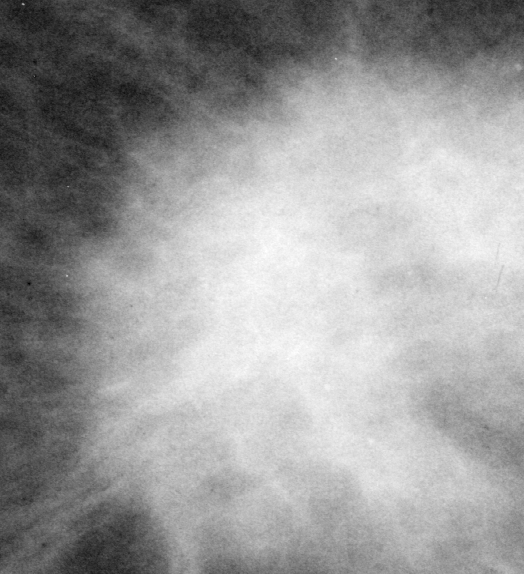
Cropped region of a digitized screen-film mammogram centred on a radiologist-marked abnormality, left breast, CC view, BI-RADS breast density category 2 (scale 1–4).
Finding: mass, shape irregular, margins spiculated; BI-RADS assessment category 5; pathology (as recorded): malignant.